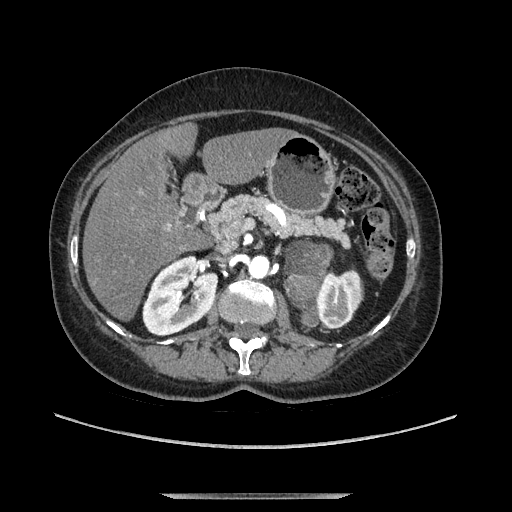
Contrast-enhanced abdominal CT, one axial slice. Position 61 of 169 along the scan axis. Soft-tissue window (W 400 / L 40 HU). 1.25 mm slice thickness. 512 × 512 image matrix. Female patient. Case-level facts recorded for this patient, not image findings: diagnosis: adrenocortical carcinoma; tumour side: left adrenal; tumour size at pathology: 9 cm; Ki-67 index: 2 %; stage (as recorded): 3.
Outlined on this slice (semi-automatically segmented with operator editing):
- mass: bounding box (x1, y1, x2, y2) in pixels: (287, 245, 332, 325)